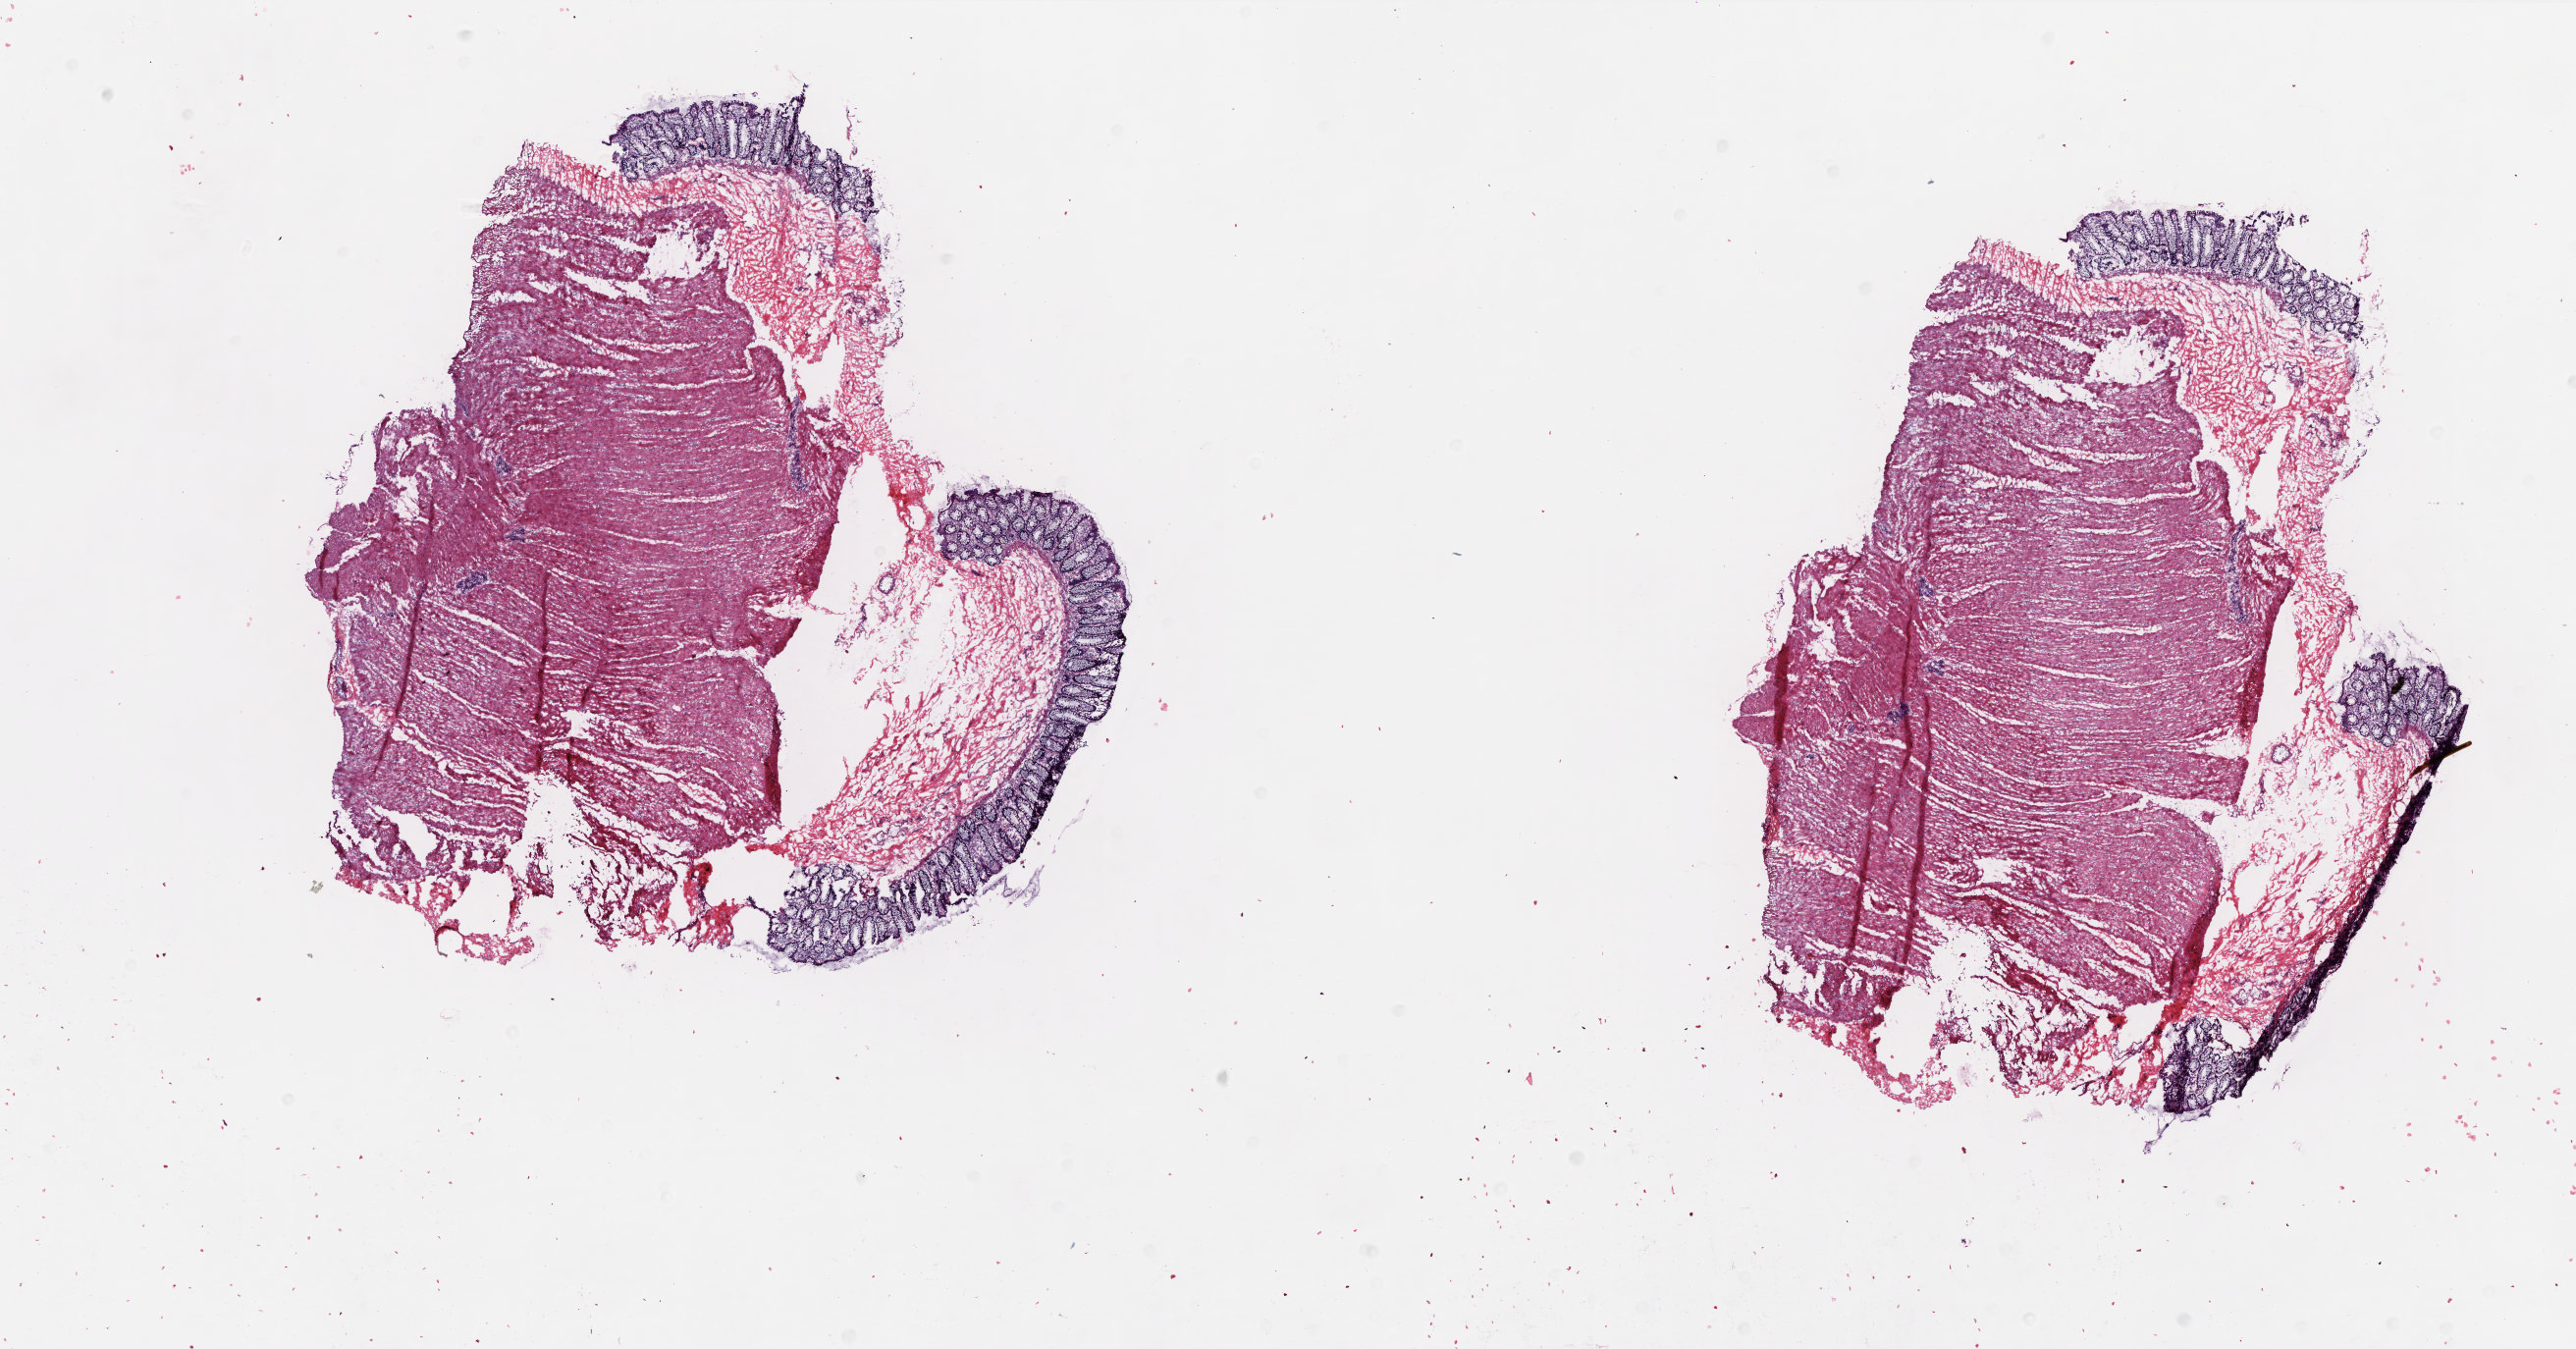
Whole-slide histology image, Hematoxylin and eosin (H&E) stained, a low-resolution overview of the entire scanned area, about 21.0 x 11.0 mm (from a 20x scan); frozen section from the bottom of the tissue portion; solid tissue normal (non-tumour tissue) sample from the colon. Patient: female, age at initial diagnosis 47 years. Slide review estimates, as recorded: tumour cells 0%, normal cells 100%. Inflammatory infiltration, as recorded: lymphocyte infiltration 20%, monocyte infiltration 3%, neutrophil infiltration 0%.
This section: solid tissue normal sample (biorepository sample class). Patient diagnosis: Adenocarcinoma, NOS (sigmoid colon).